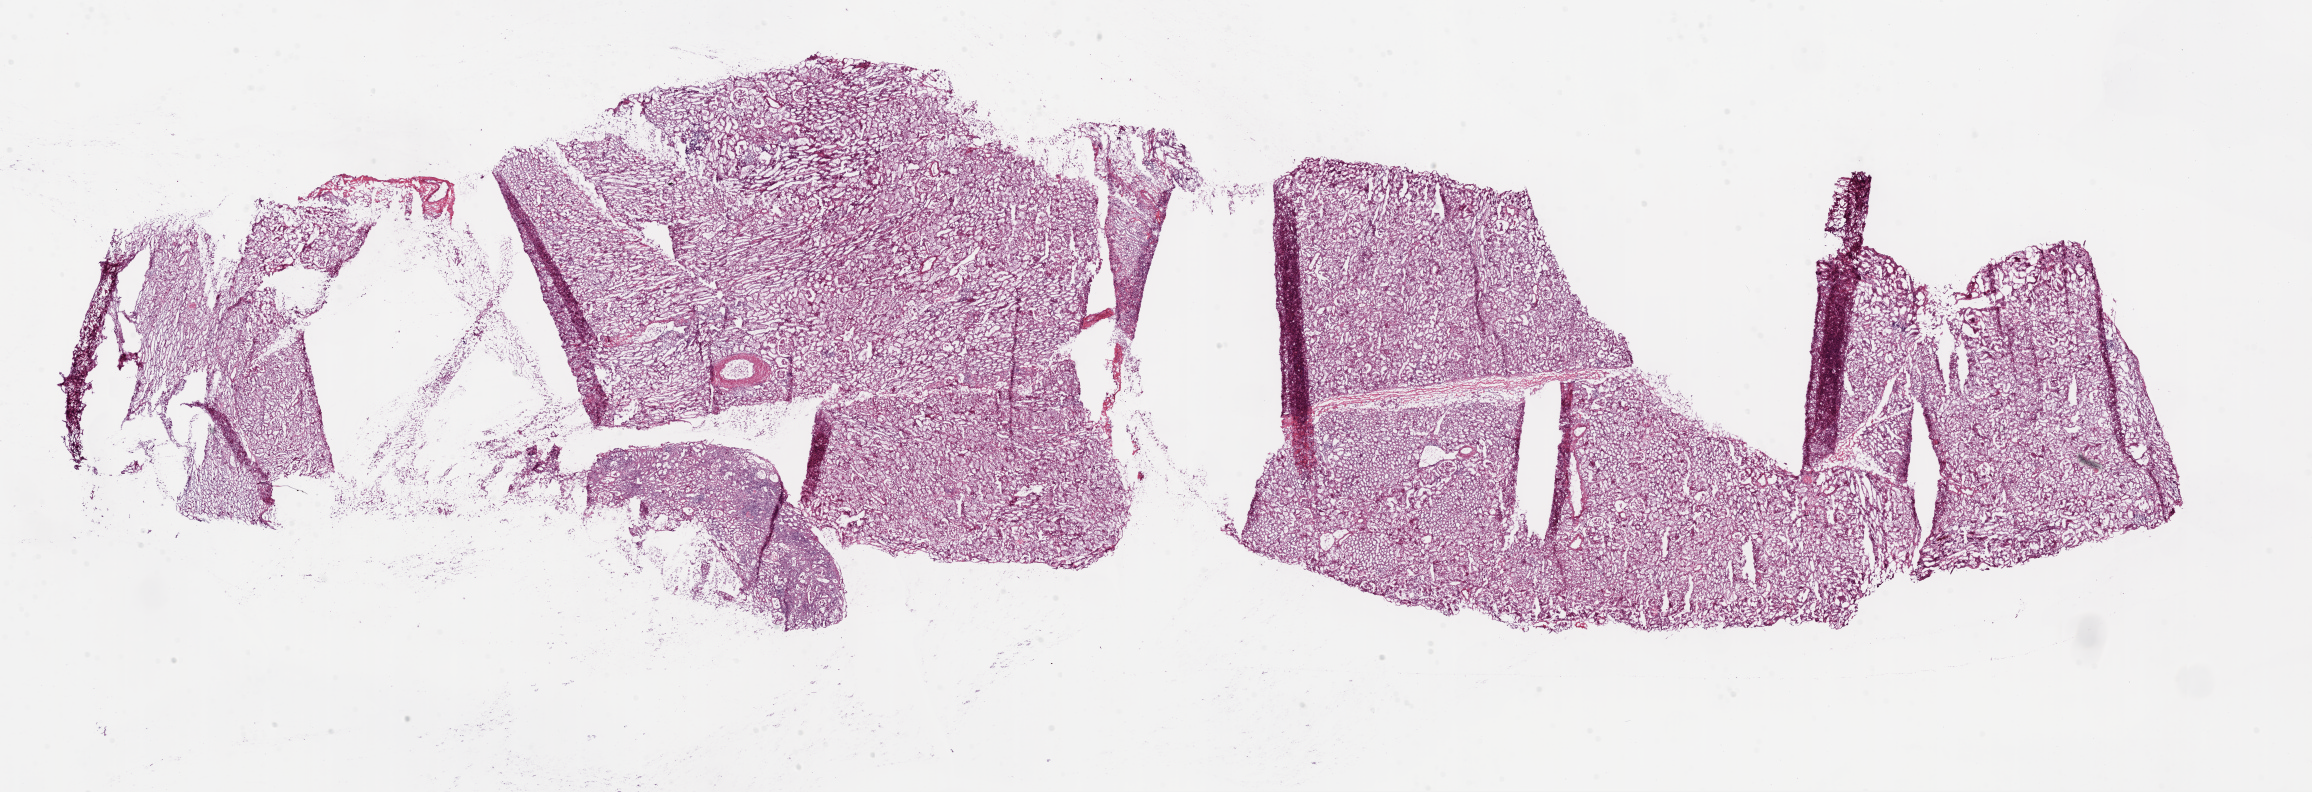
H&E whole-slide image, shown as a low-resolution overview of the whole scanned area (about 37.1 x 12.7 mm, acquisition: 20x scan), frozen section, sample: solid tissue normal (non-tumour tissue), kidney. Patient: male, age at initial diagnosis 51 years.
This section: solid tissue normal sample (biorepository sample class). Patient diagnosis: Clear cell adenocarcinoma, NOS.